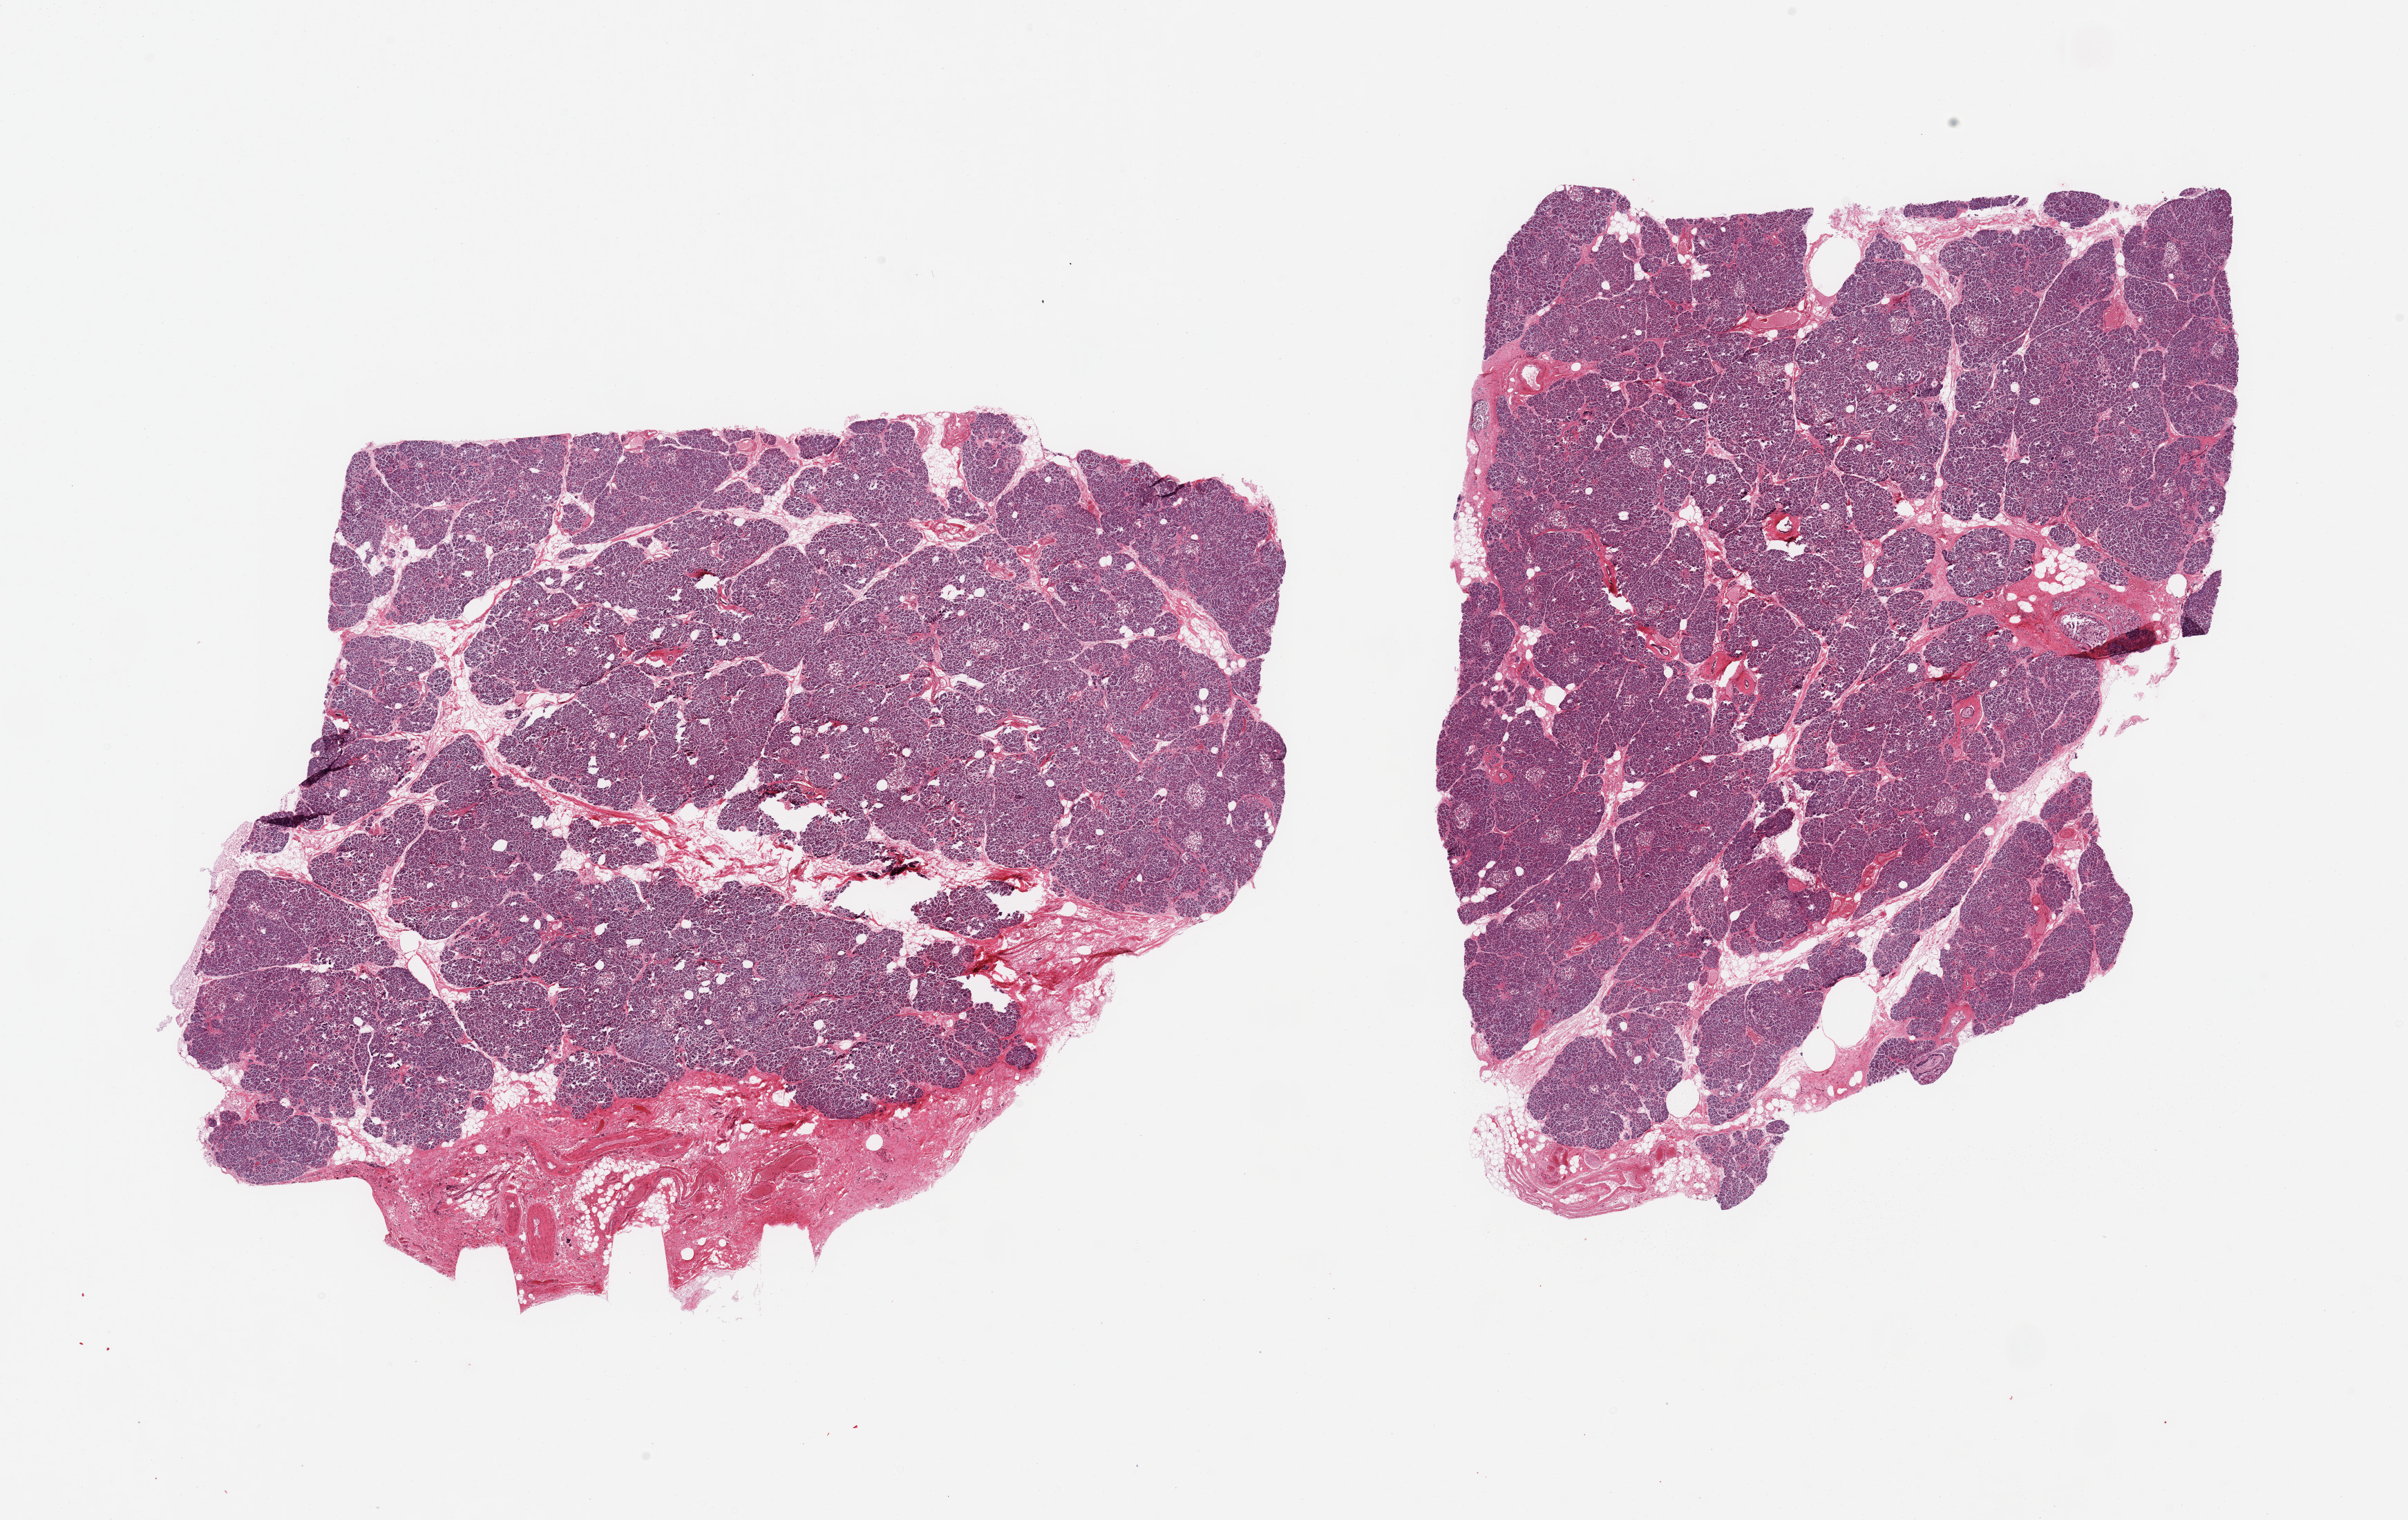
Whole-slide image, hematoxylin and eosin (H&E) stain — low-resolution overview of the scanned area, about 27.6 x 17.4 mm, PAXgene-fixed, paraffin-embedded tissue, target tissue: pancreas, donor tissue sample. Female donor.
Reviewer comment on this tissue sample: 2 pieces, islets still visible, advanced degenerative changes; Moderate parenchymal autolysis.